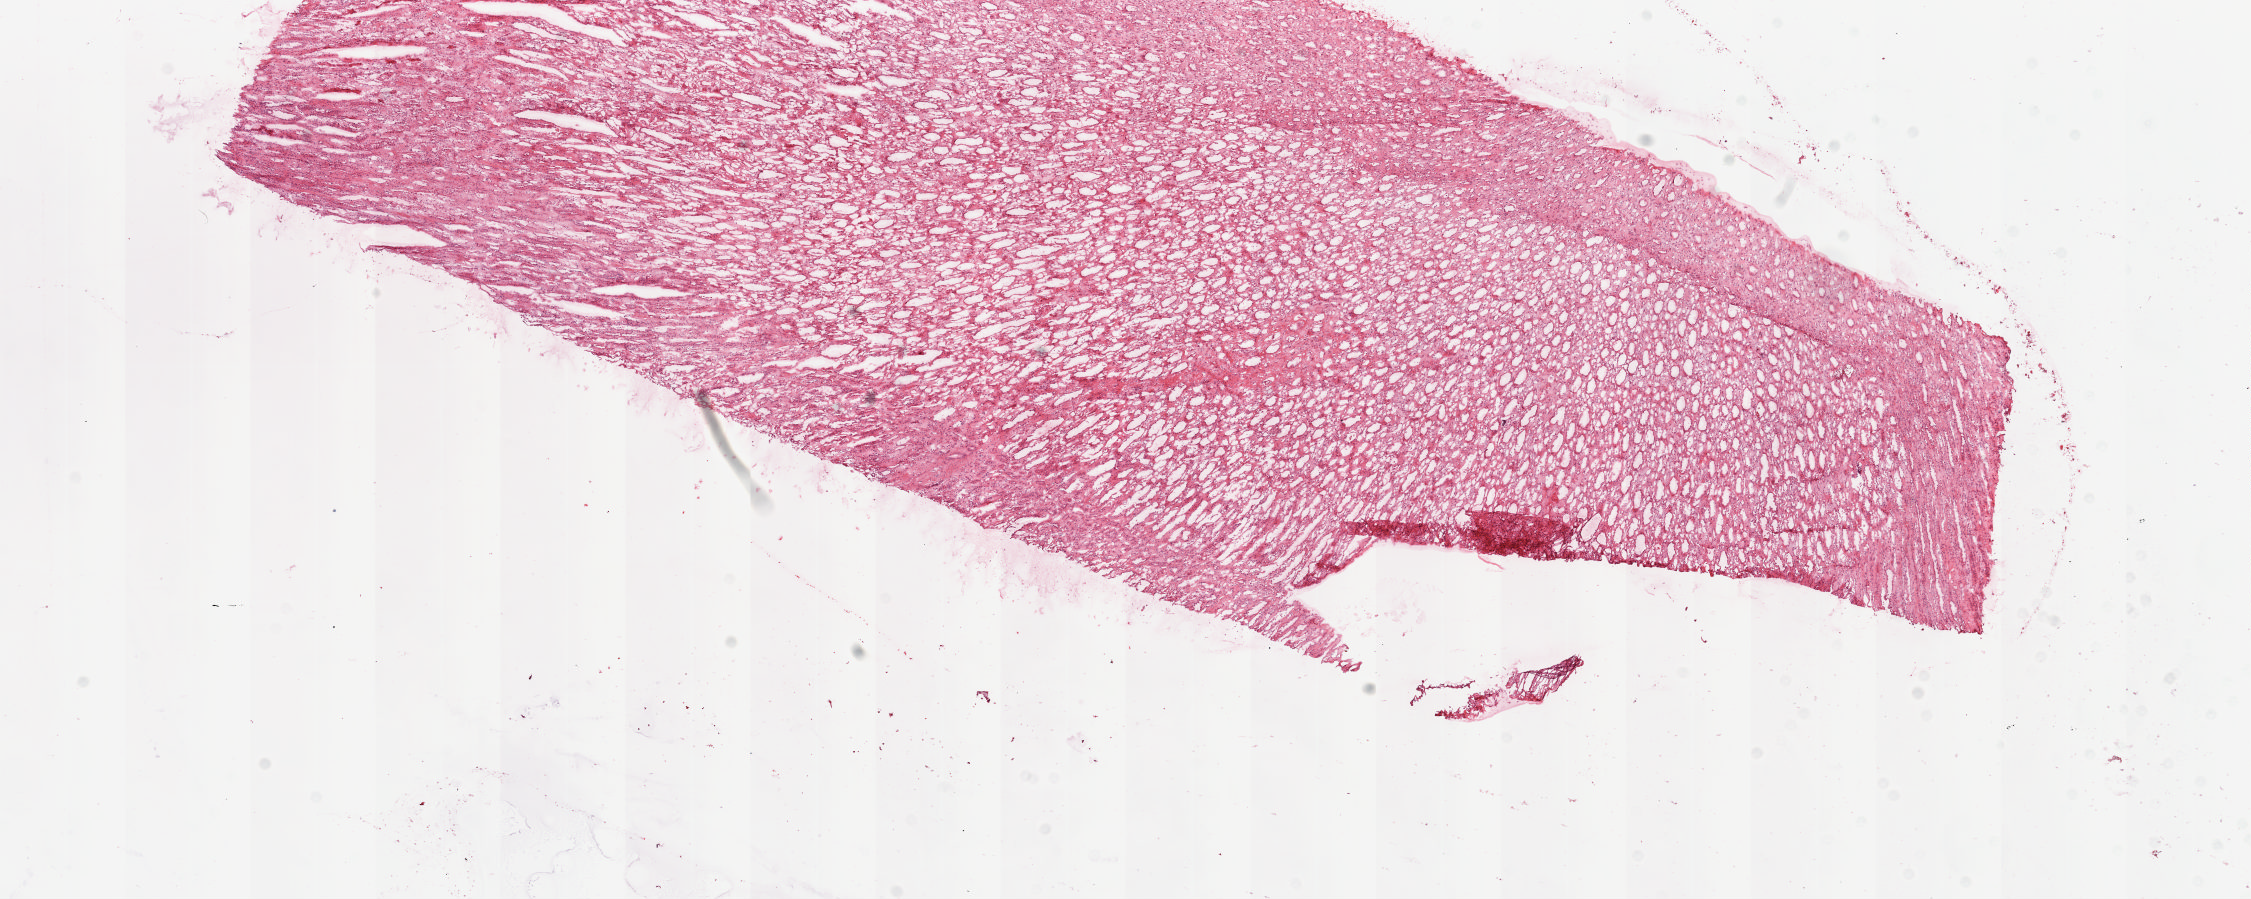
Whole-slide histology image, H&E-stained, low-resolution overview of the scanned area, about 17.9 x 7.1 mm. Frozen section. Sample: solid tissue normal (non-tumour tissue), kidney. Male, age 46 years at initial diagnosis.
• this section: solid tissue normal sample (biorepository sample class)
• patient diagnosis: Clear cell adenocarcinoma, NOS